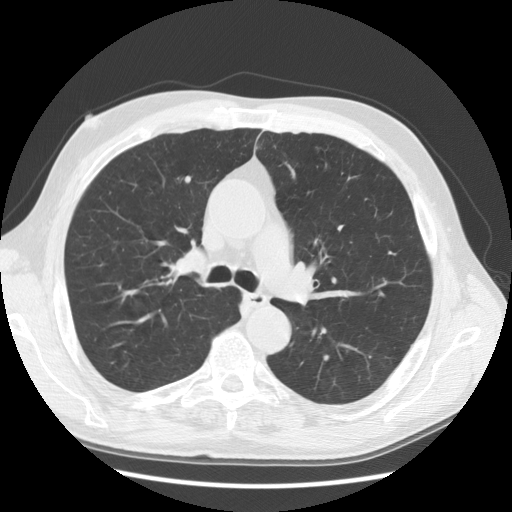
Axial slice from a low-dose chest CT screening exam. Baseline annual screen. Lung window (W 1500 / L -600 HU). 140 kVp. Slice 55 of 145 in the series. Male participant, aged 60 years at enrolment. Current smoker at enrolment.
Expert reader's lesion annotation, bounding box [x1, y1, x2, y2] px = [158, 231, 215, 284]. No non-calcified nodule or mass ≥4 mm was recorded by the screening reader at this exam. Later outcome: lung cancer diagnosed 193 days after this screen — squamous cell carcinoma, NOS, right upper lobe, moderately differentiated (G2), stage IIIB (AJCC 6th edition), 52 mm at pathology.